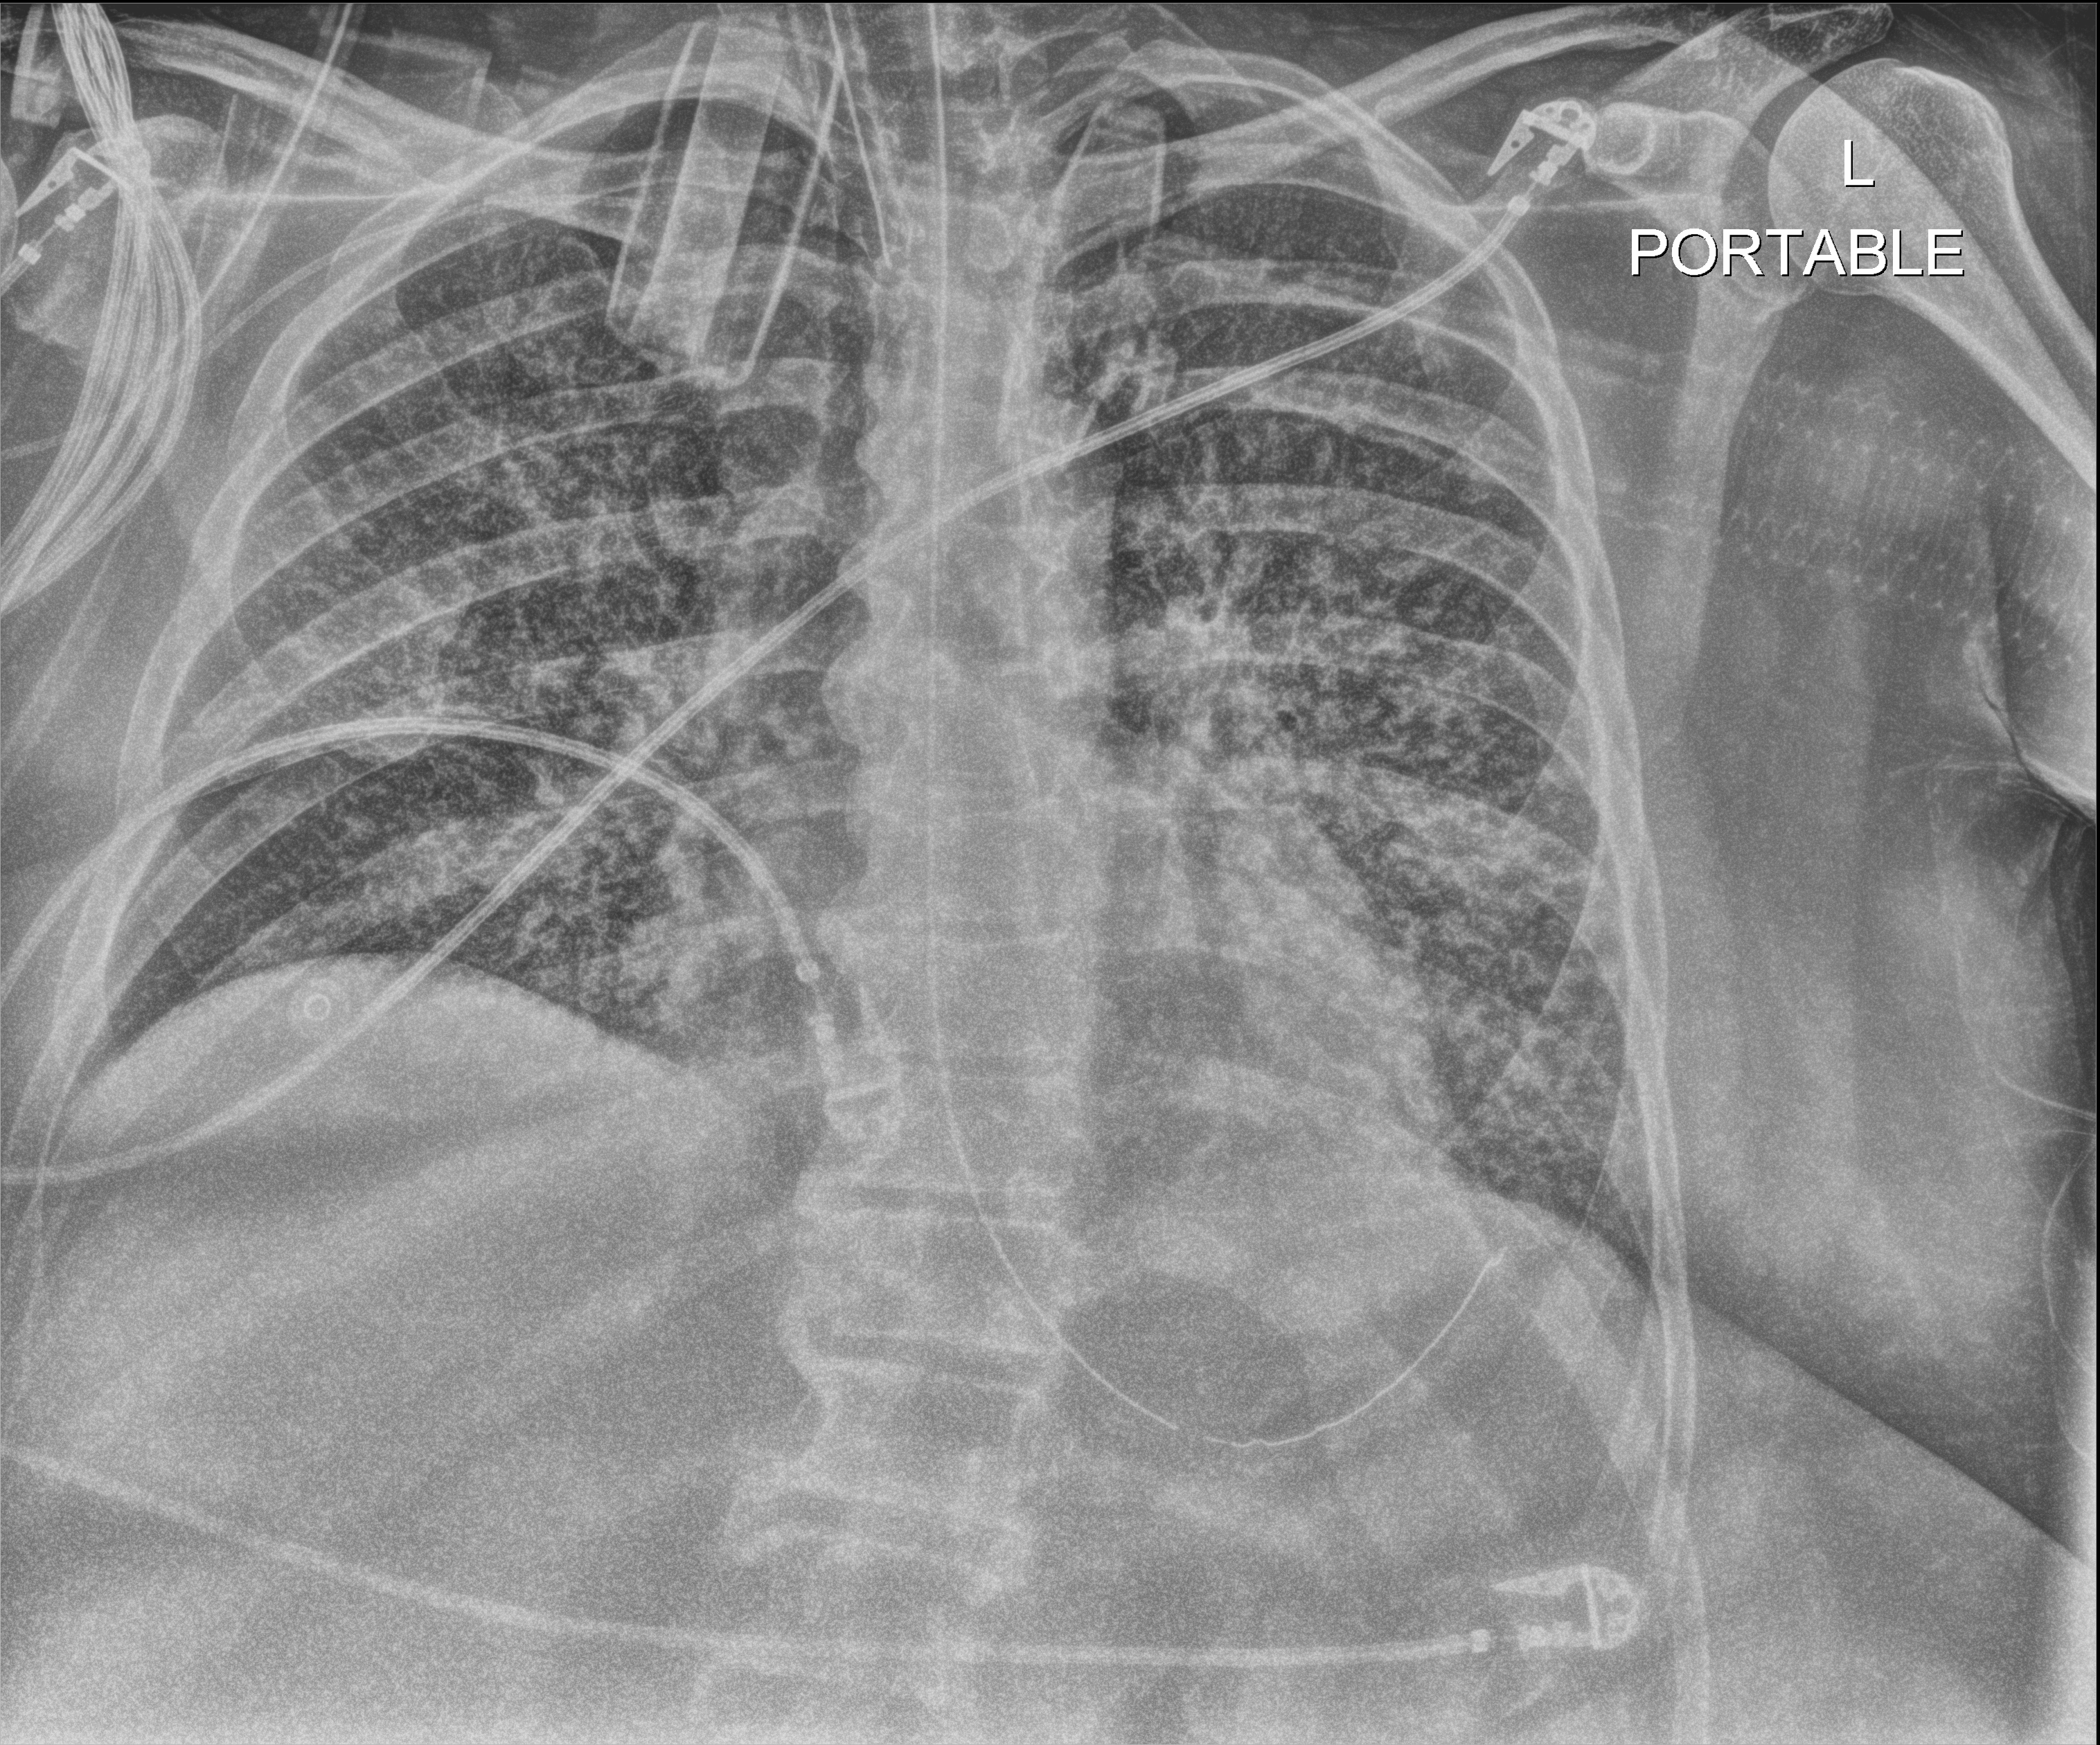
Chest X-ray, anteroposterior (AP) projection. Adult patient hospitalised with COVID-19, age 18–59 years.
From the hospital-stay record, not from the radiograph (when in the stay this image was taken is not recorded): admitted to intensive care during this hospital stay: yes; length of hospital stay: 28 days.